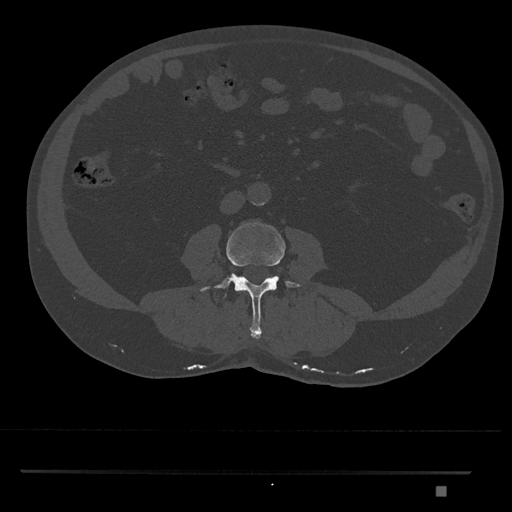
CT including the spine, one axial slice; slice 676 of 1134 in the series (ordered by position); 120 kVp; bone window (W 1800 / L 400 HU); 512 × 512 image matrix, field of view 429 × 429 mm. Male patient, age 65 years. Case-level facts recorded for this patient, not image findings: primary cancer: prostate.
Outlined on this slice (semi-automatic segmentation, software-assisted and operator-edited):
- L3 vertebra: bounding box [x1, y1, x2, y2] px = [200, 222, 302, 339]